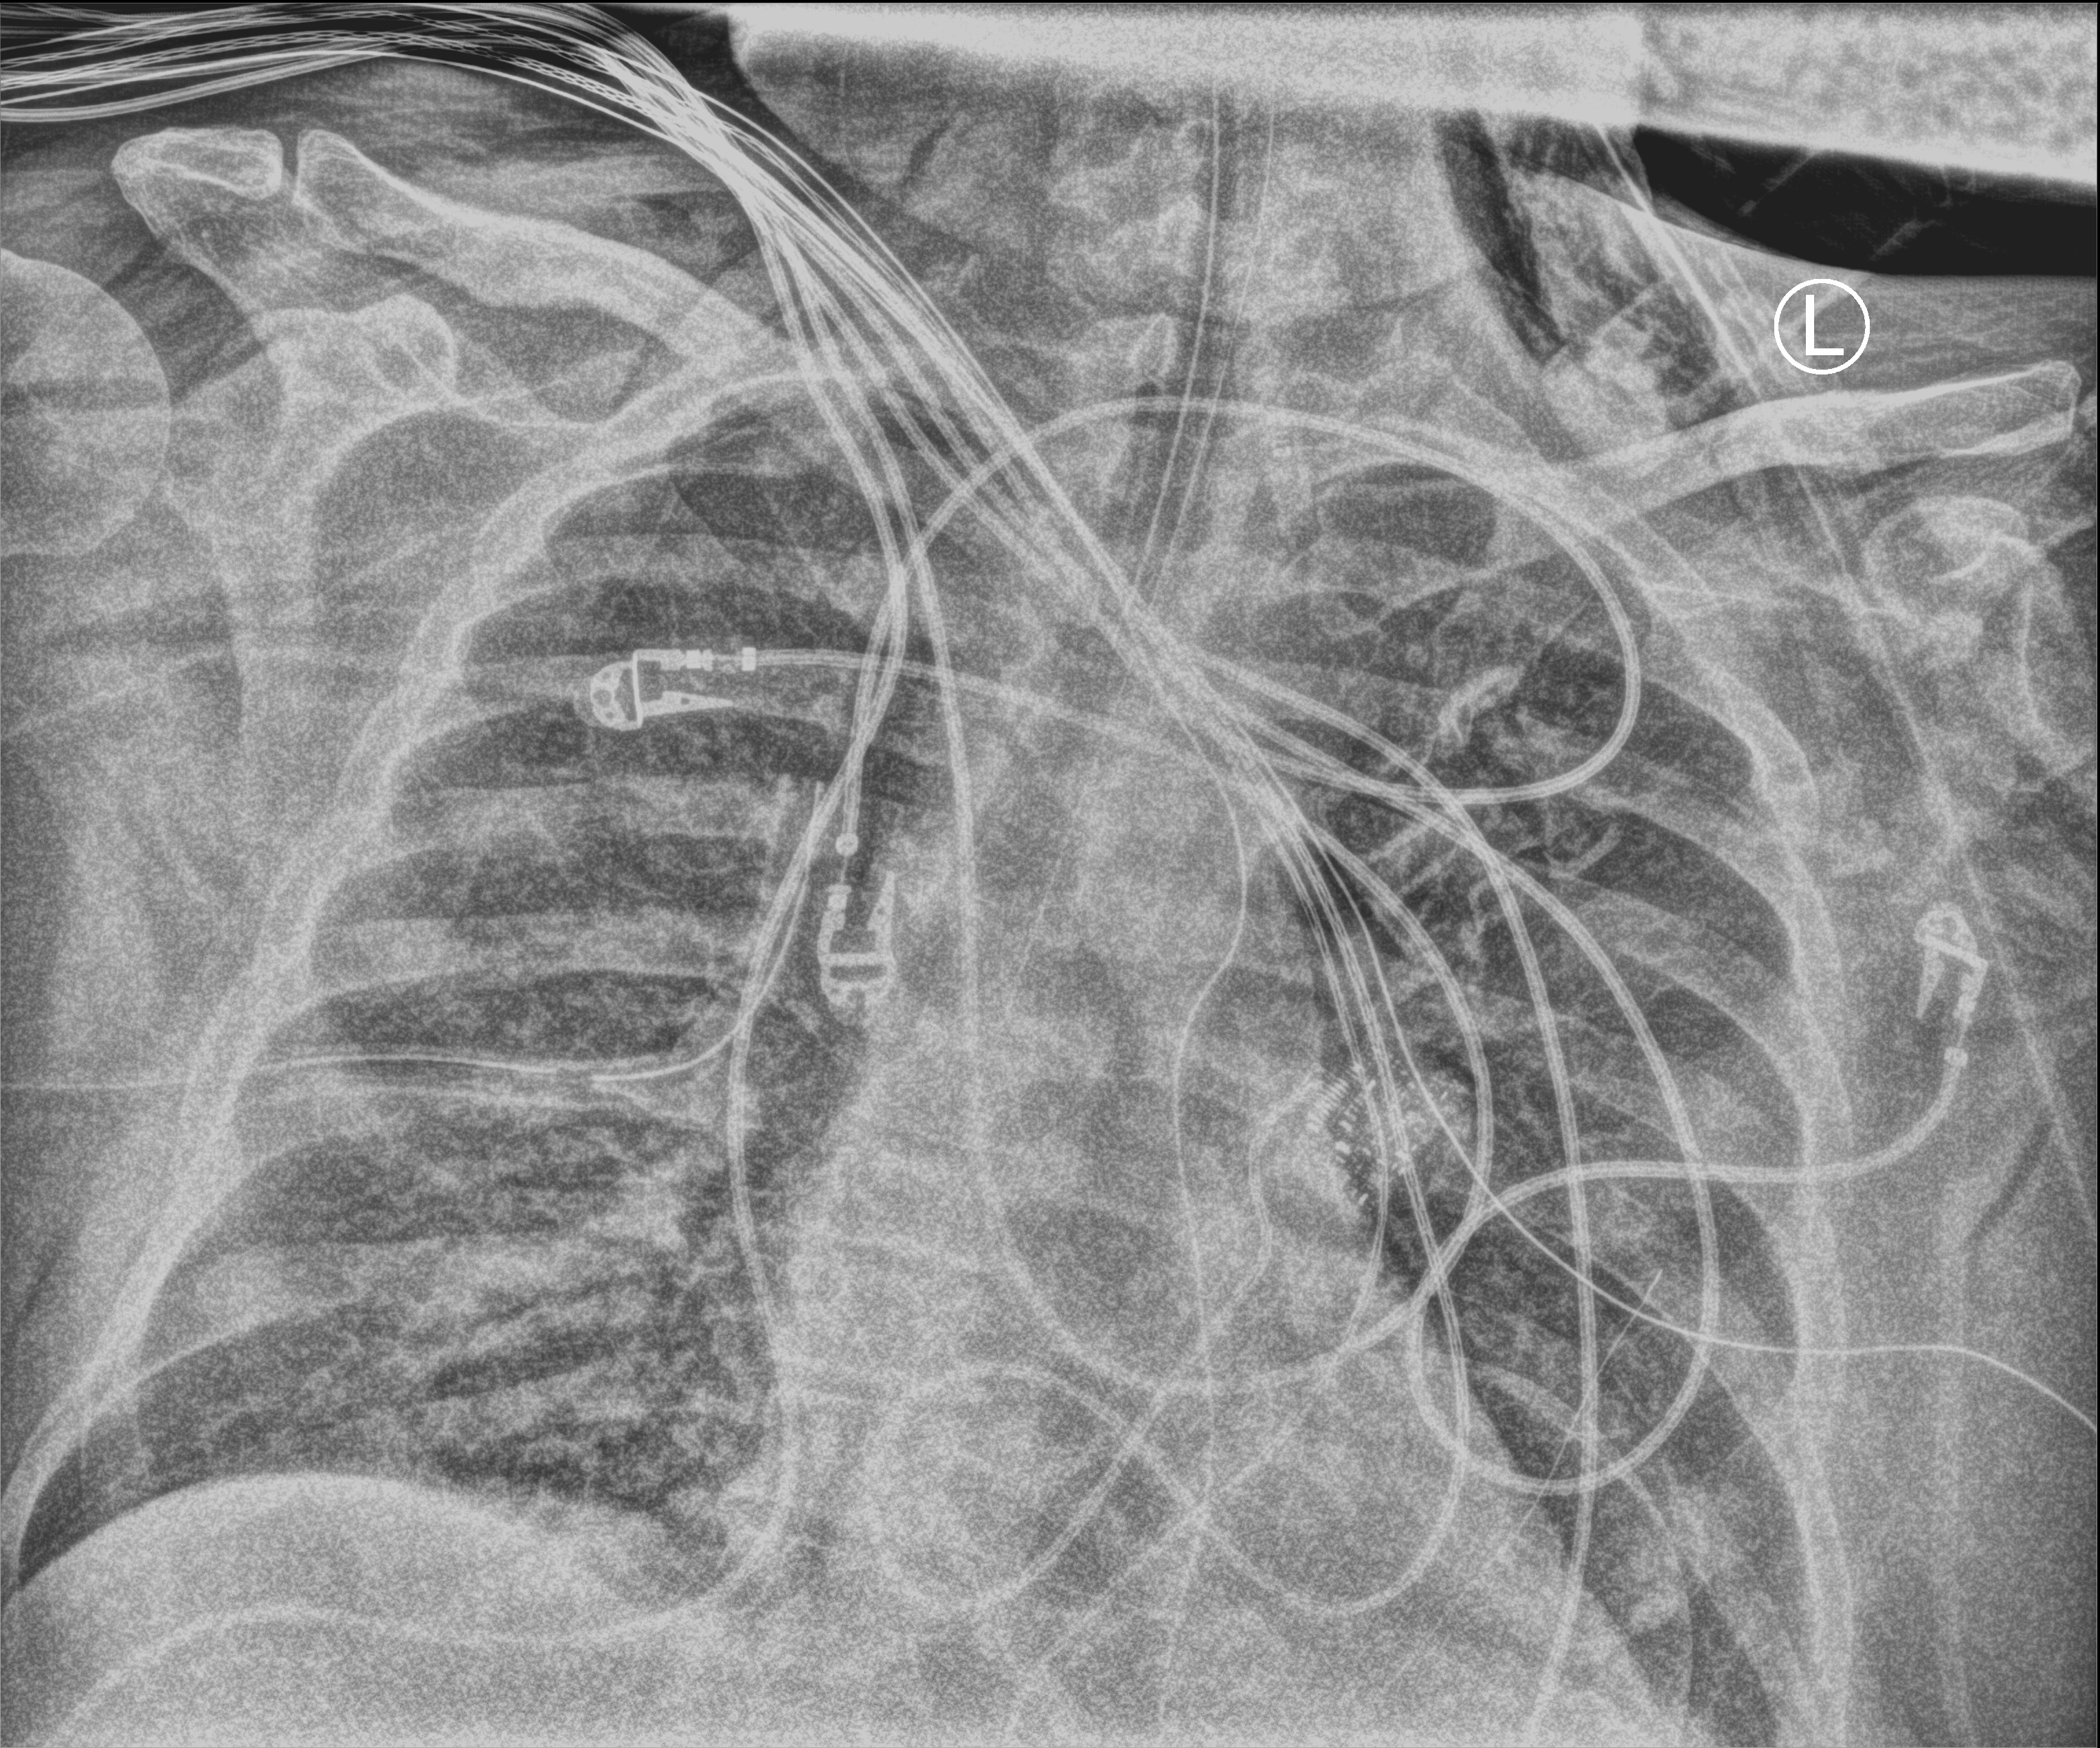
Portable chest radiograph; anteroposterior (AP) projection. Adult patient hospitalised with COVID-19, age 18–59 years.
Hospital-stay facts (about this admission, not read from this image; timing relative to this image not recorded):
- admitted to intensive care during this hospital stay: yes